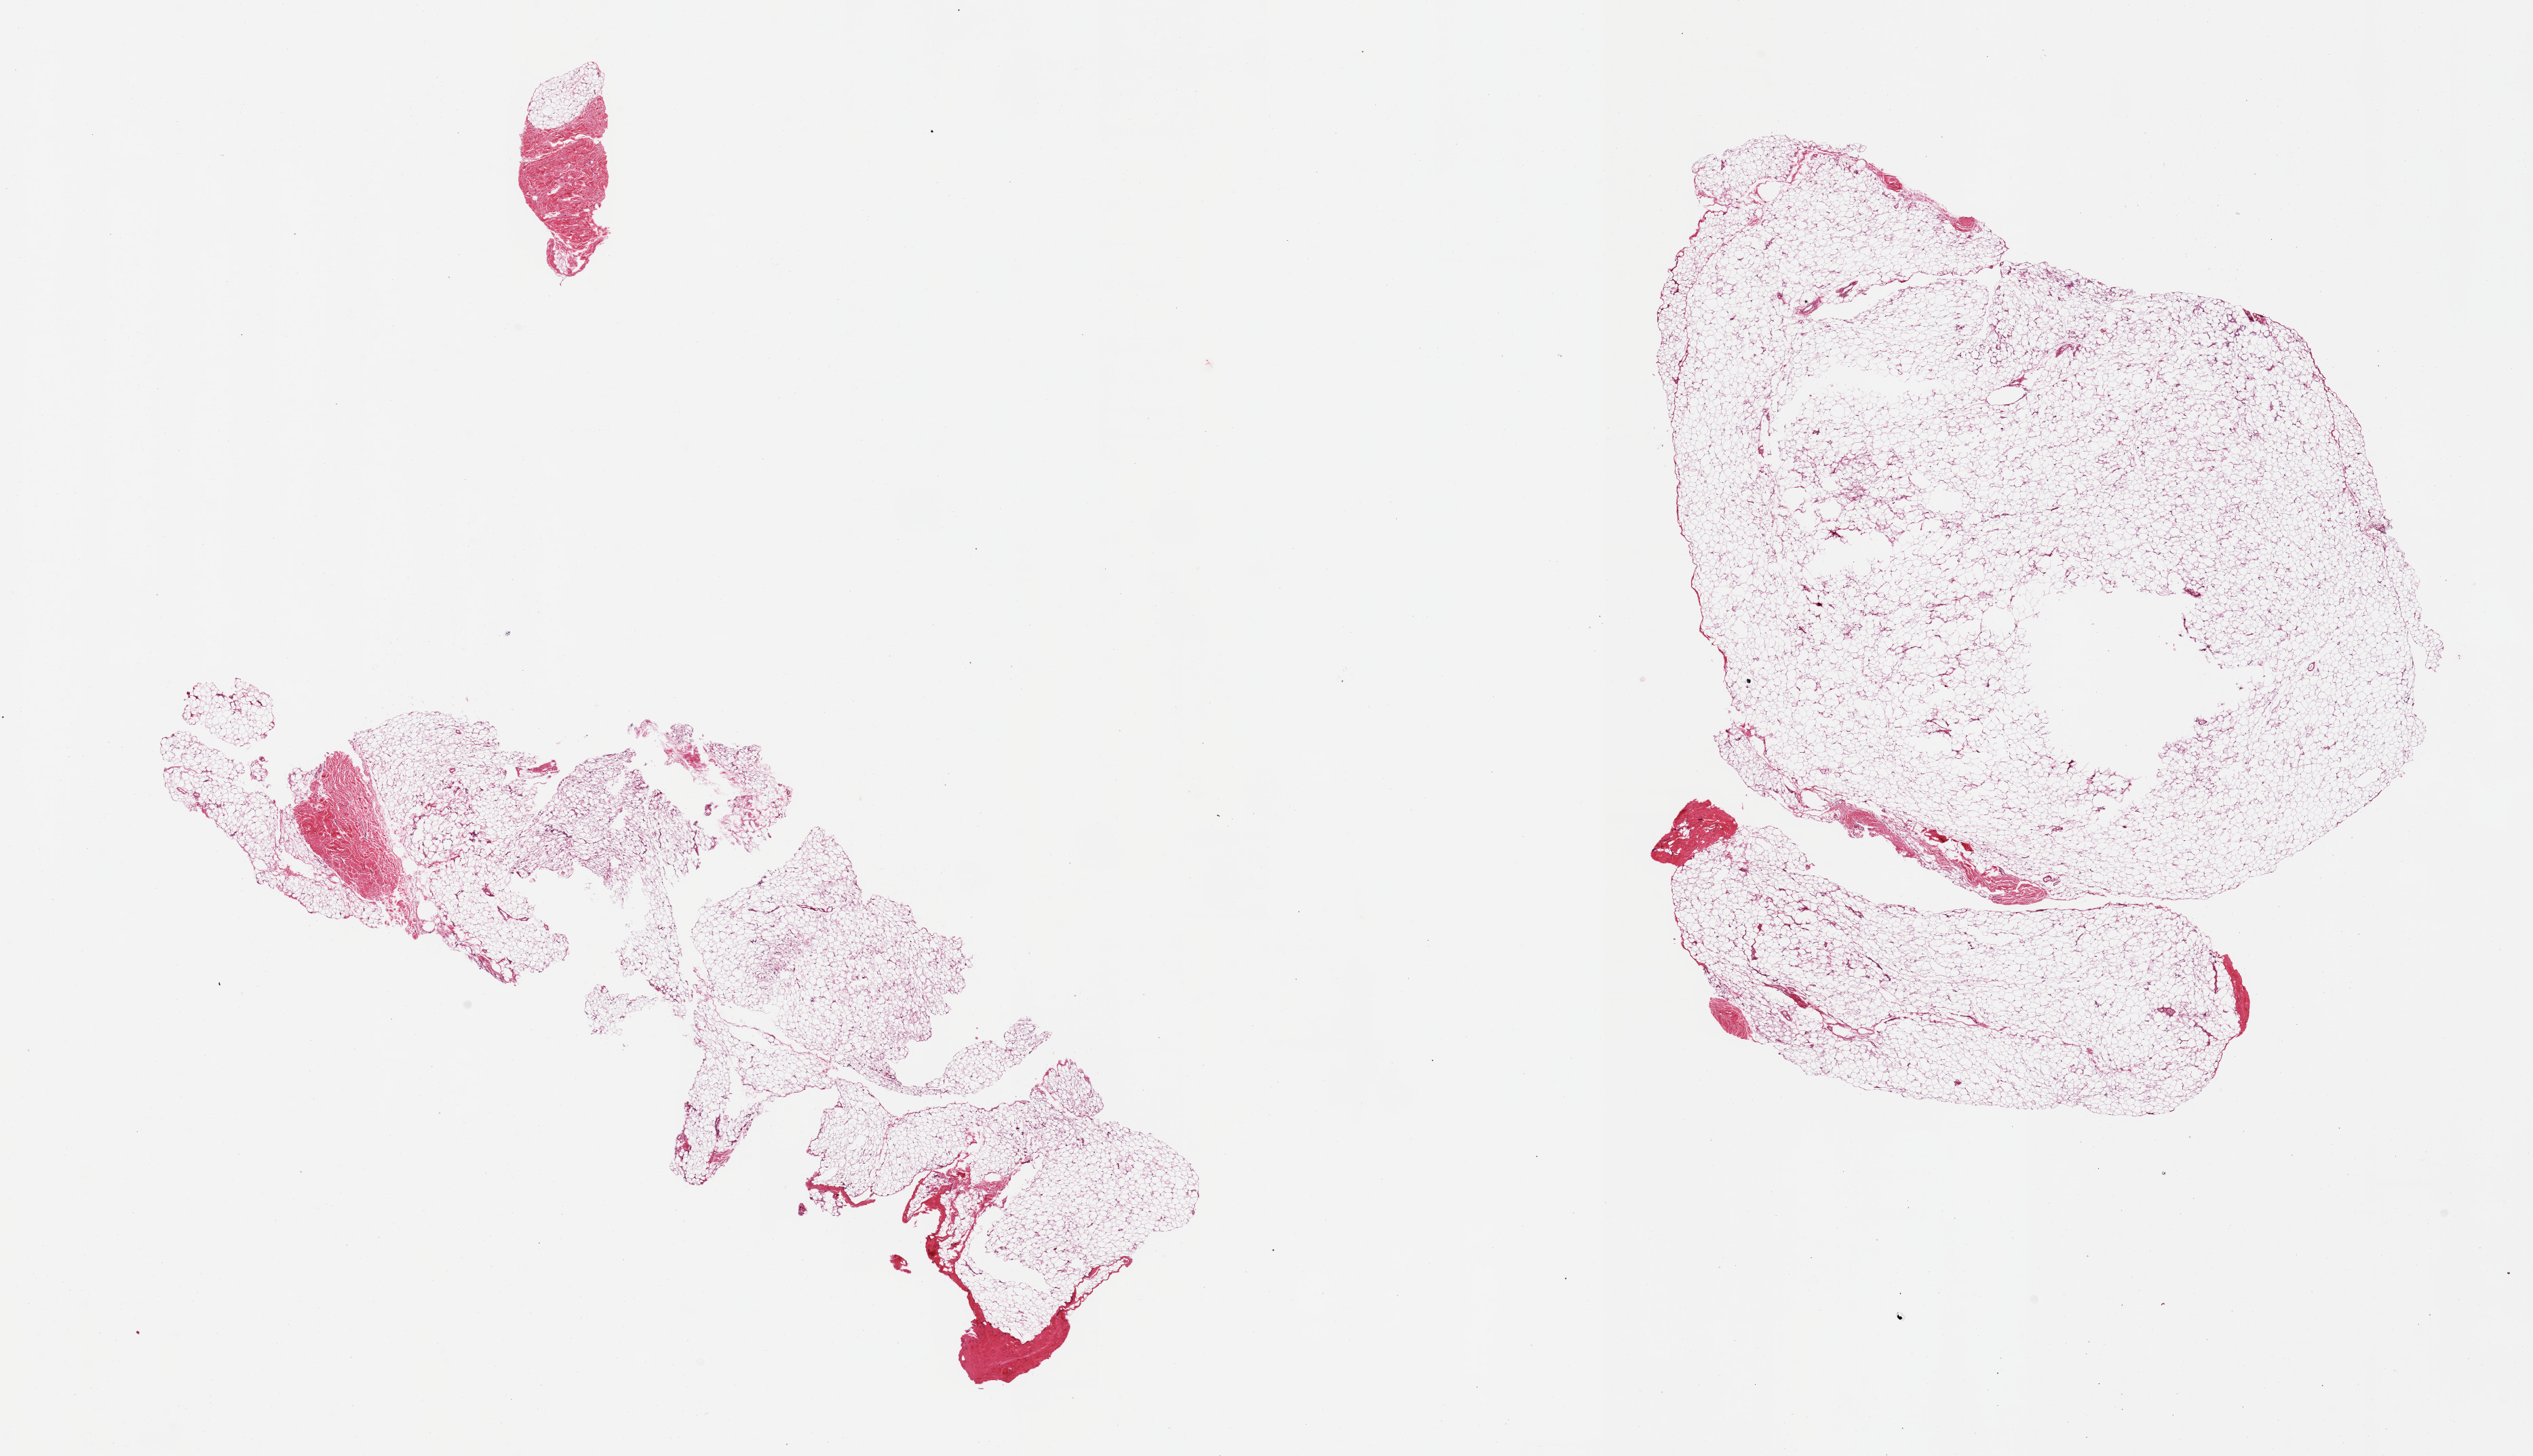
Hematoxylin and eosin (H&E) whole-slide image — shown as a low-resolution overview of the whole scanned area (about 29.5 x 17.0 mm), PAXgene-fixed paraffin-embedded (PFPE) section, target tissue: breast, donor tissue sample. Female donor.
Reviewer comment on this tissue sample: 2 pieces, adipose elements, trace fibrous tissue.